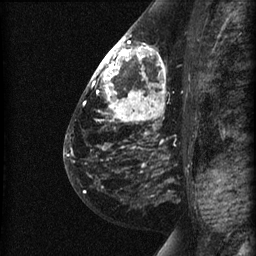
Breast MRI (dynamic contrast-enhanced), one sagittal slice. Position 34 of 60 along the scan axis. Dynamic contrast-enhanced series, image 2 of 3 at this slice position (ordered by acquisition). 1.5 T. TE 4.2 ms, TR 22.7 ms. 1.5 mm slice thickness. 256 × 256 image matrix. Female patient, age 48 years. Case-level facts recorded for this patient, not image findings: setting: breast cancer imaged before/during neoadjuvant chemotherapy; receptor status: triple-negative.
Structures marked on this image (semi-automatically segmented with operator editing):
- analysis volume of interest (the breast-tissue region the enhancement analysis was run in; not a lesion): bounding box [x1, y1, x2, y2] px = [89, 27, 191, 180]
- tumour enhancement mask (voxels above the 90 % enhancement threshold inside the analysis volume of interest): [93, 37, 164, 111]